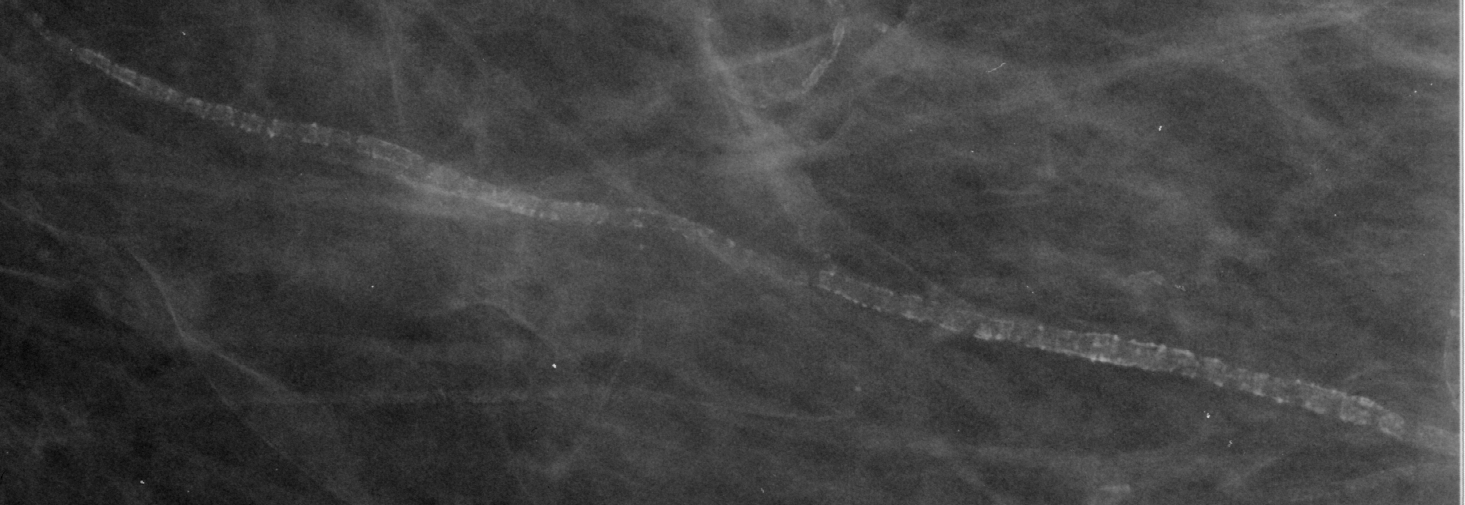
Crop from a digitized film mammogram around one marked abnormality; right breast; CC view.
Finding: calcifications, morphology vascular; BI-RADS assessment category 2; benign without callback (not worked up further).